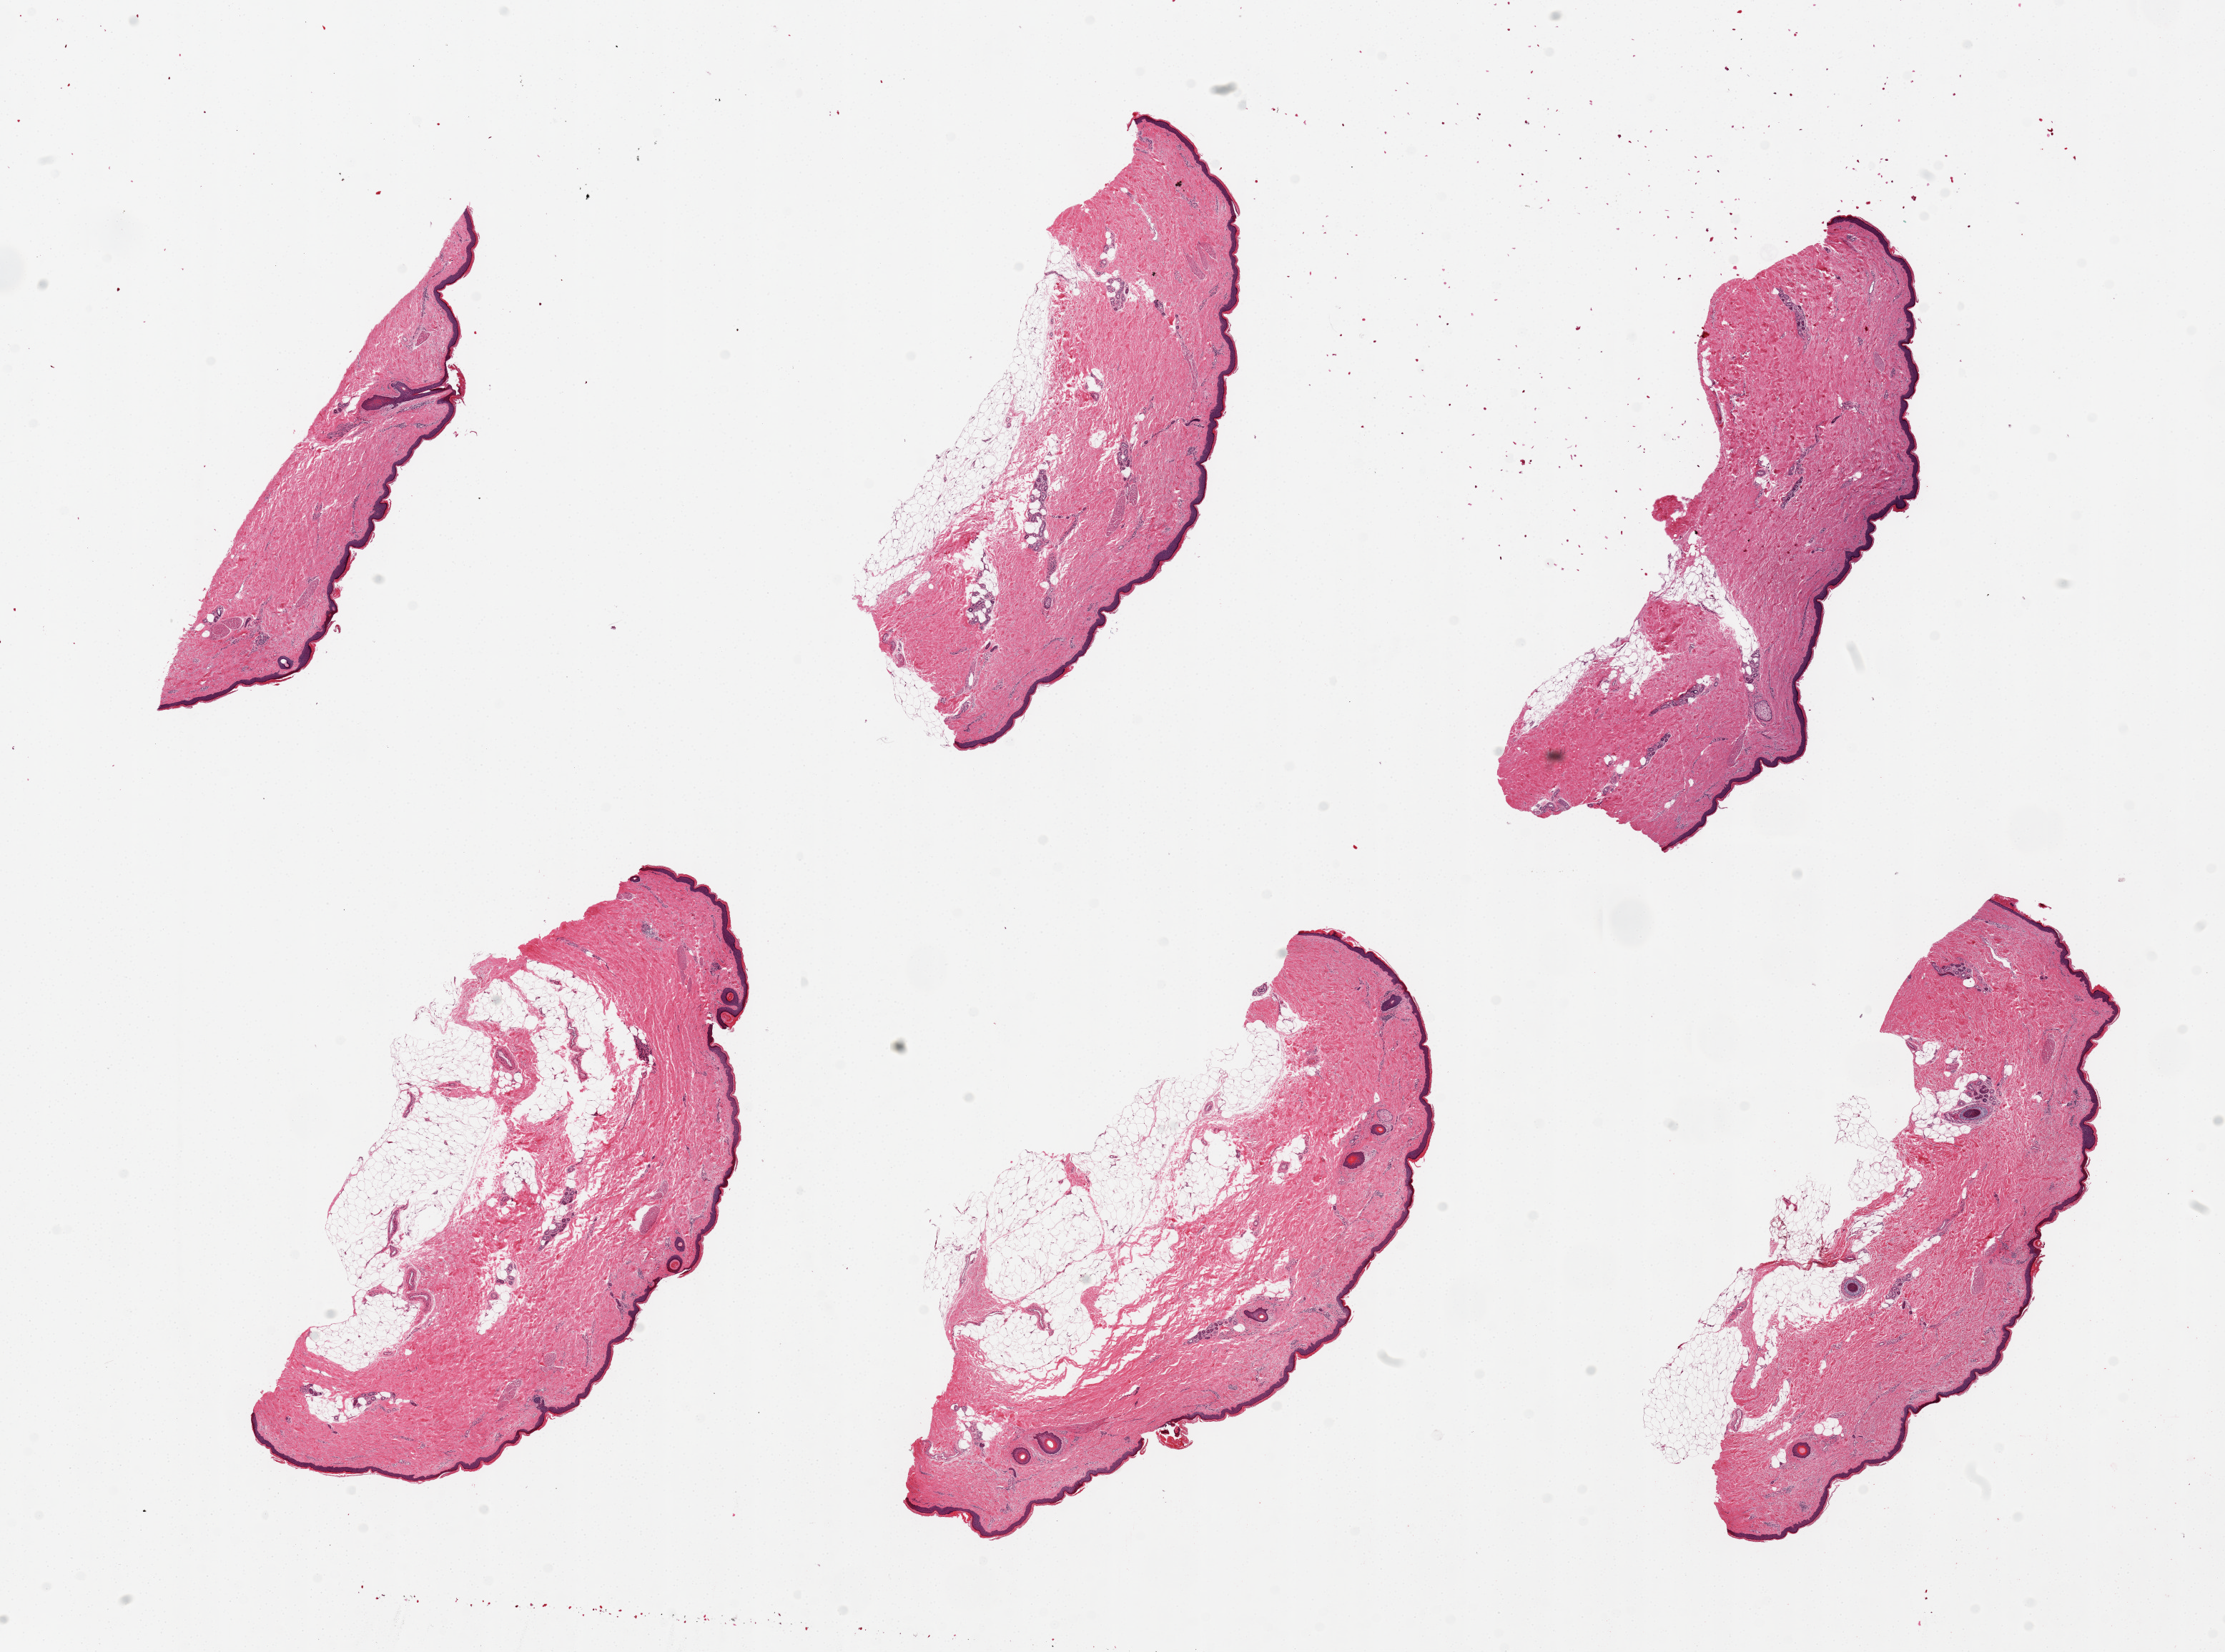
Digitized hematoxylin and eosin (H&E)-stained section — low-resolution overview of the scanned area, about 24.6 x 18.3 mm, PAXgene-fixed paraffin-embedded (PFPE) section, sampled site (target tissue): skin of lower leg, donor tissue sample. Donor: male.
Reviewer comment on this tissue sample: 6 pieces, squamous epithelium is ~80 microns thick.